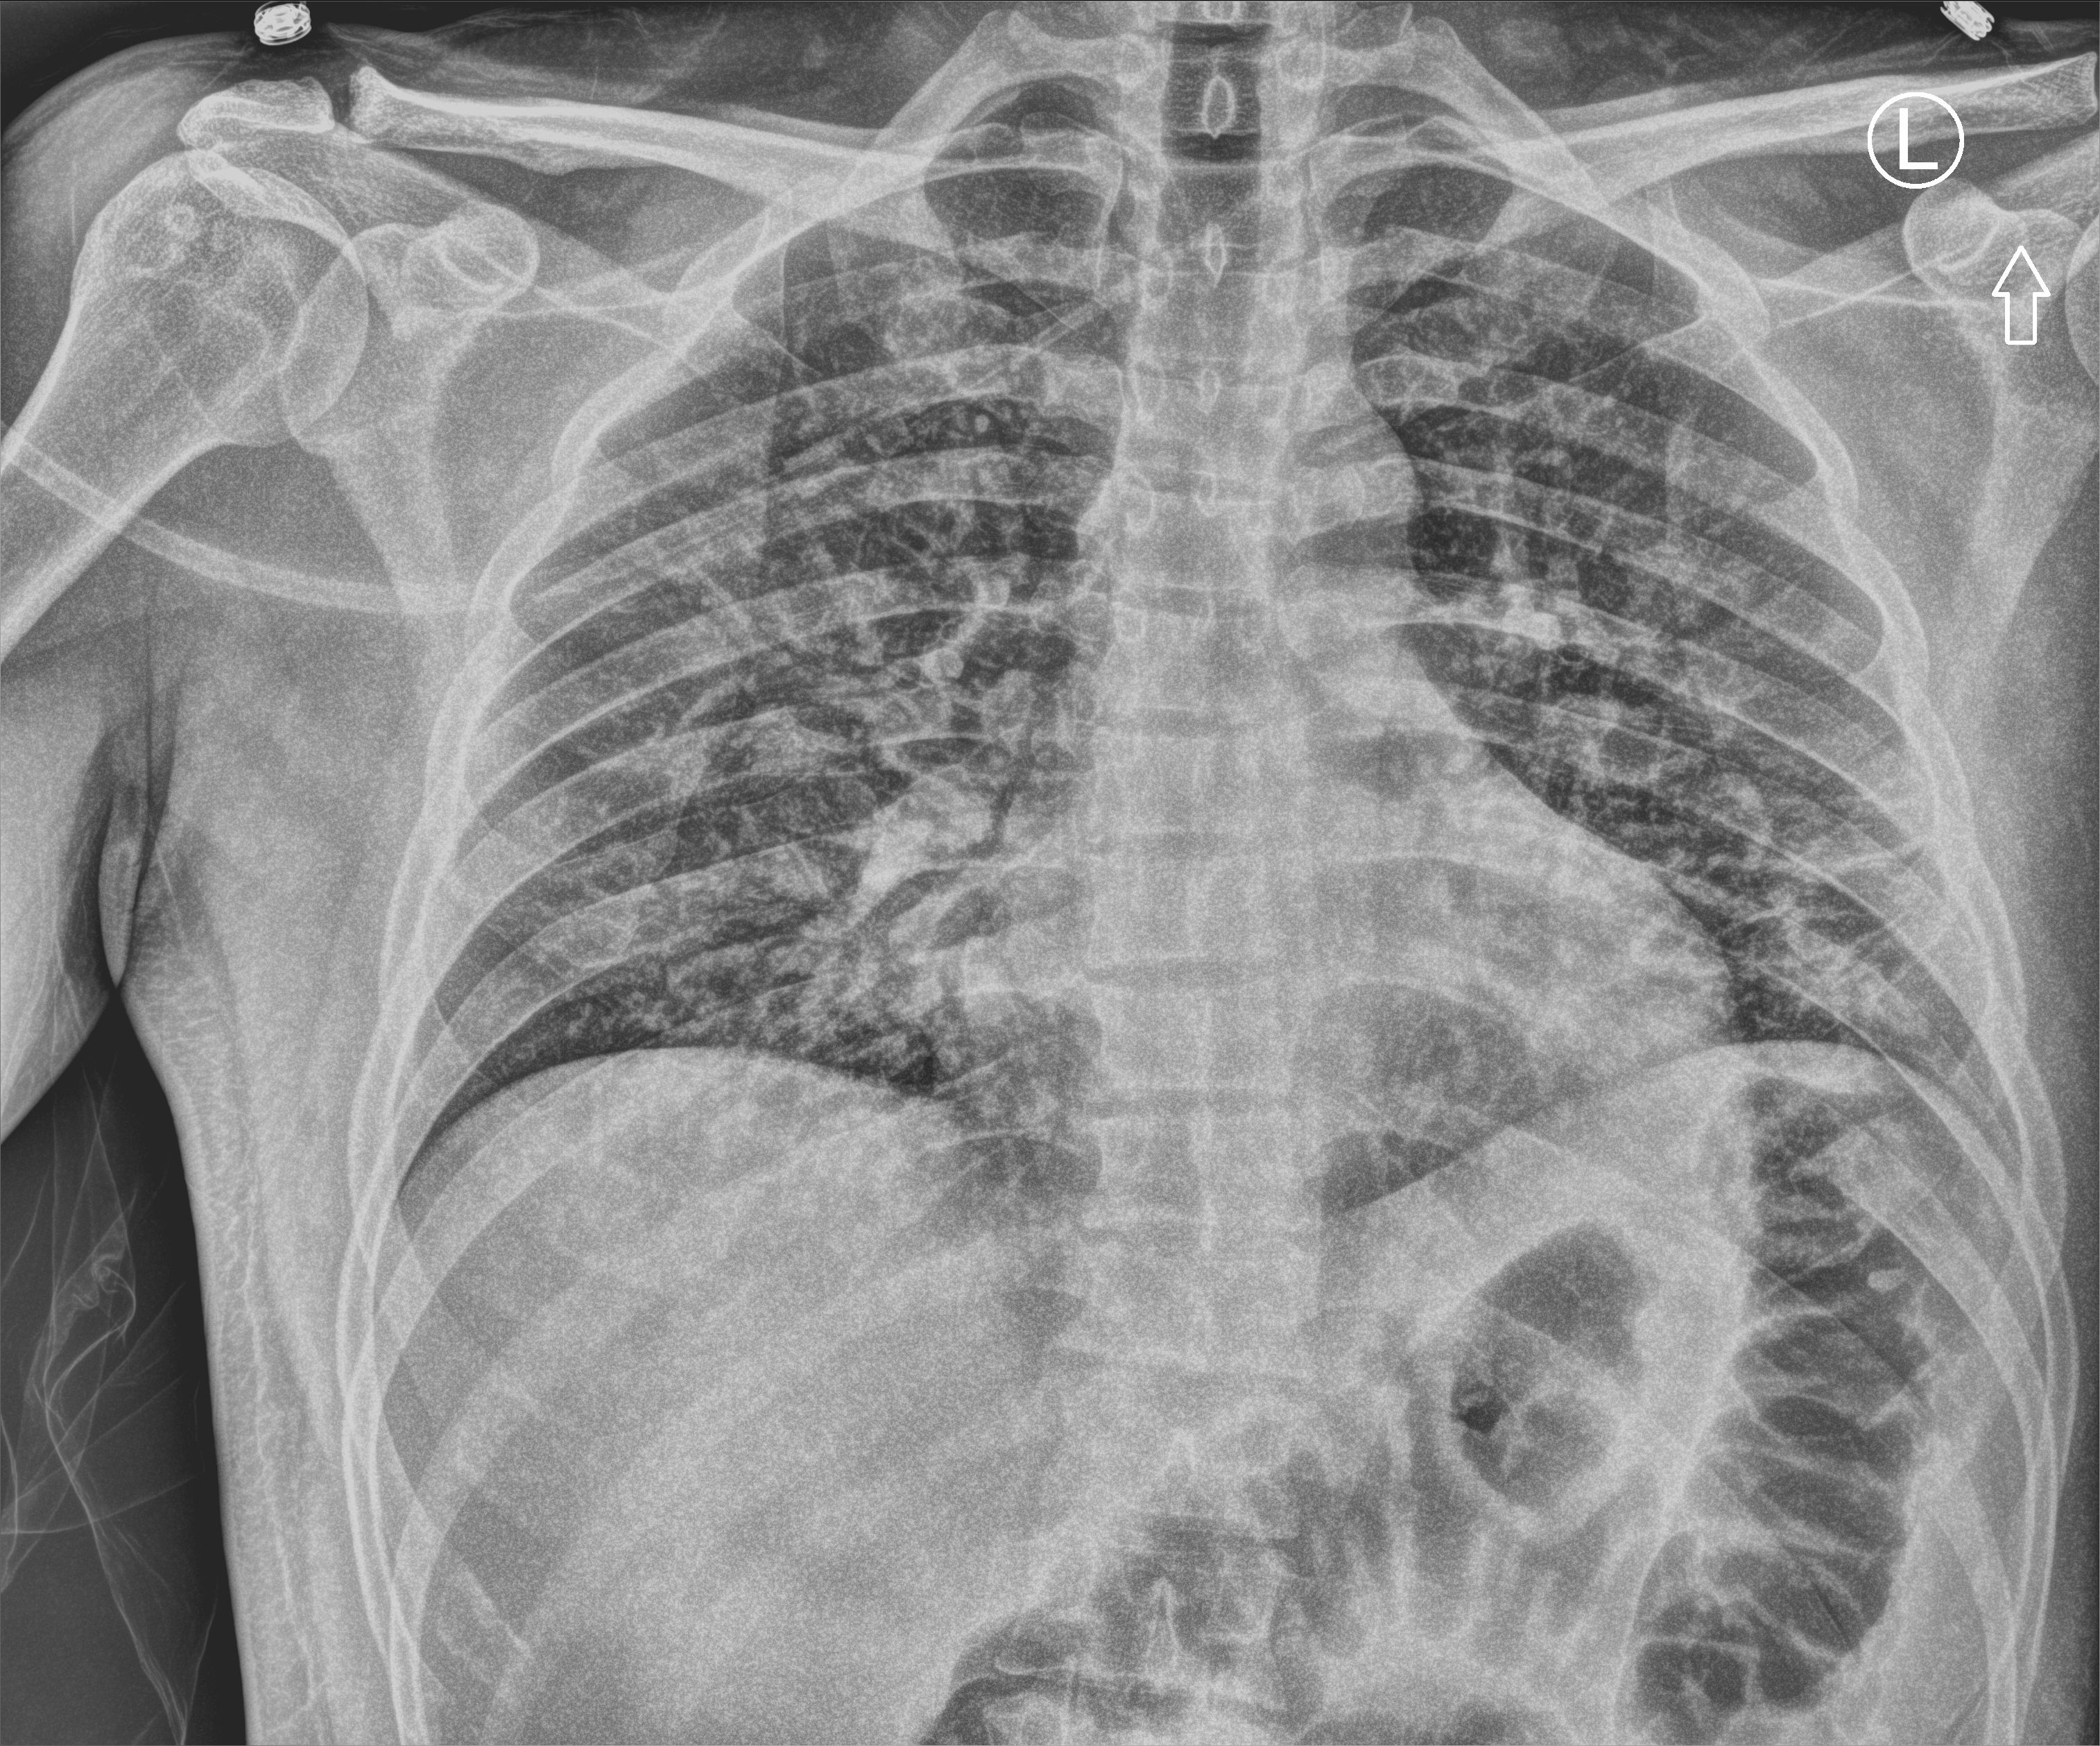
Chest X-ray (portable), anteroposterior (AP) projection. Patient hospitalised with COVID-19; male, aged 18–59 years.
From the hospital-stay record, not from the radiograph (when in the stay this image was taken is not recorded): mechanically ventilated during this hospital stay: no; admitted to intensive care during this hospital stay: no.